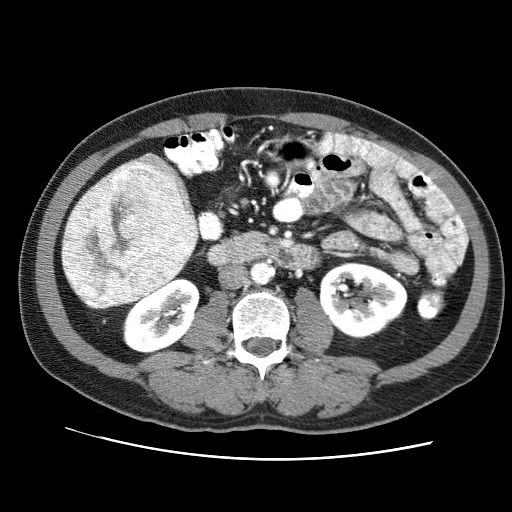
Contrast-enhanced abdominal CT (liver protocol), one axial slice. Position 19 of 71 along the scan axis. 120 kVp. Soft-tissue window (W 400 / L 40 HU). 2.5 mm slice thickness. 512 × 512 image matrix, field of view 360 × 360 mm. Case-level facts recorded for this patient, not image findings: diagnosis: hepatocellular carcinoma (patient treated with transarterial chemoembolisation; whether this scan precedes or follows treatment is not stated here); TNM stage (as recorded): Stage-II; Child-Pugh class: A; tumour nodularity: multinodular; tumour size: 4.6 cm.
Annotated regions visible in this slice (semi-automatically segmented with operator editing):
- liver parenchyma outside the tumour (the mass and vessels are separate outlines, so this box may not span the whole liver): bounding box <61,154,196,309> (left, top, right, bottom; pixels)
- mass: <61,160,197,309>
- liver vessels: <120,167,123,170>